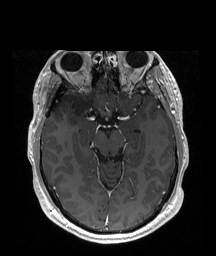
Brain MRI from a brain-tumour surgery series, one axial slice; position 119 of 192 along the scan axis; T1-weighted post-contrast; 216 × 256 image matrix. Case-level facts recorded for this patient, not image findings: histopathology: Astrocytoma; WHO grade: 2; IDH mutation: yes; tumour location: Right Insular.
Annotated regions visible in this slice (outlined manually by an expert reader):
- tumour: bounding box <67,93,90,126> (left, top, right, bottom; pixels)